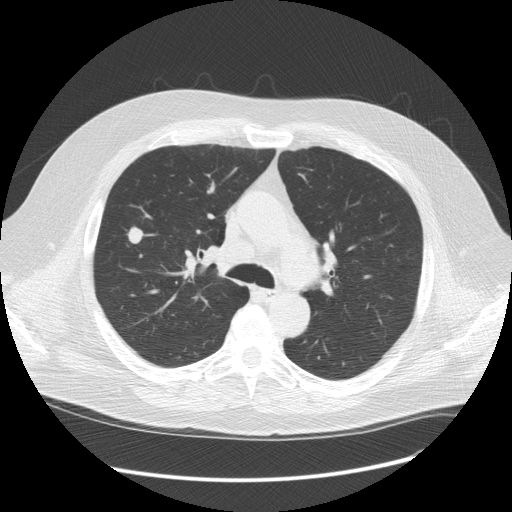
Chest CT (low-dose screening protocol), one axial image; third screening round (two years after baseline); lung window (W 1500 / L -600 HU); slice 43 of 128 in the series; 512 × 512 image matrix. Male, age 61 years at enrolment. Current smoker at enrolment.
- Lesion marked by an expert reader, bounding box (x1, y1, x2, y2) in pixels: (108, 218, 151, 257).
- Reader record for this screening exam (exam-level; its link to the box is not recorded): non-calcified nodule or mass ≥4 mm, right upper lobe, 13 × 11 mm, spiculated (stellate) margins, soft tissue attenuation, pre-existing on the prior screen: yes; interval growth: yes.
- Official screen result: positive, other.
- Later outcome: lung cancer diagnosed 21 days after this screen — adenocarcinoma, NOS, right upper lobe, stage IIIA (AJCC 6th edition), 13 mm at pathology.